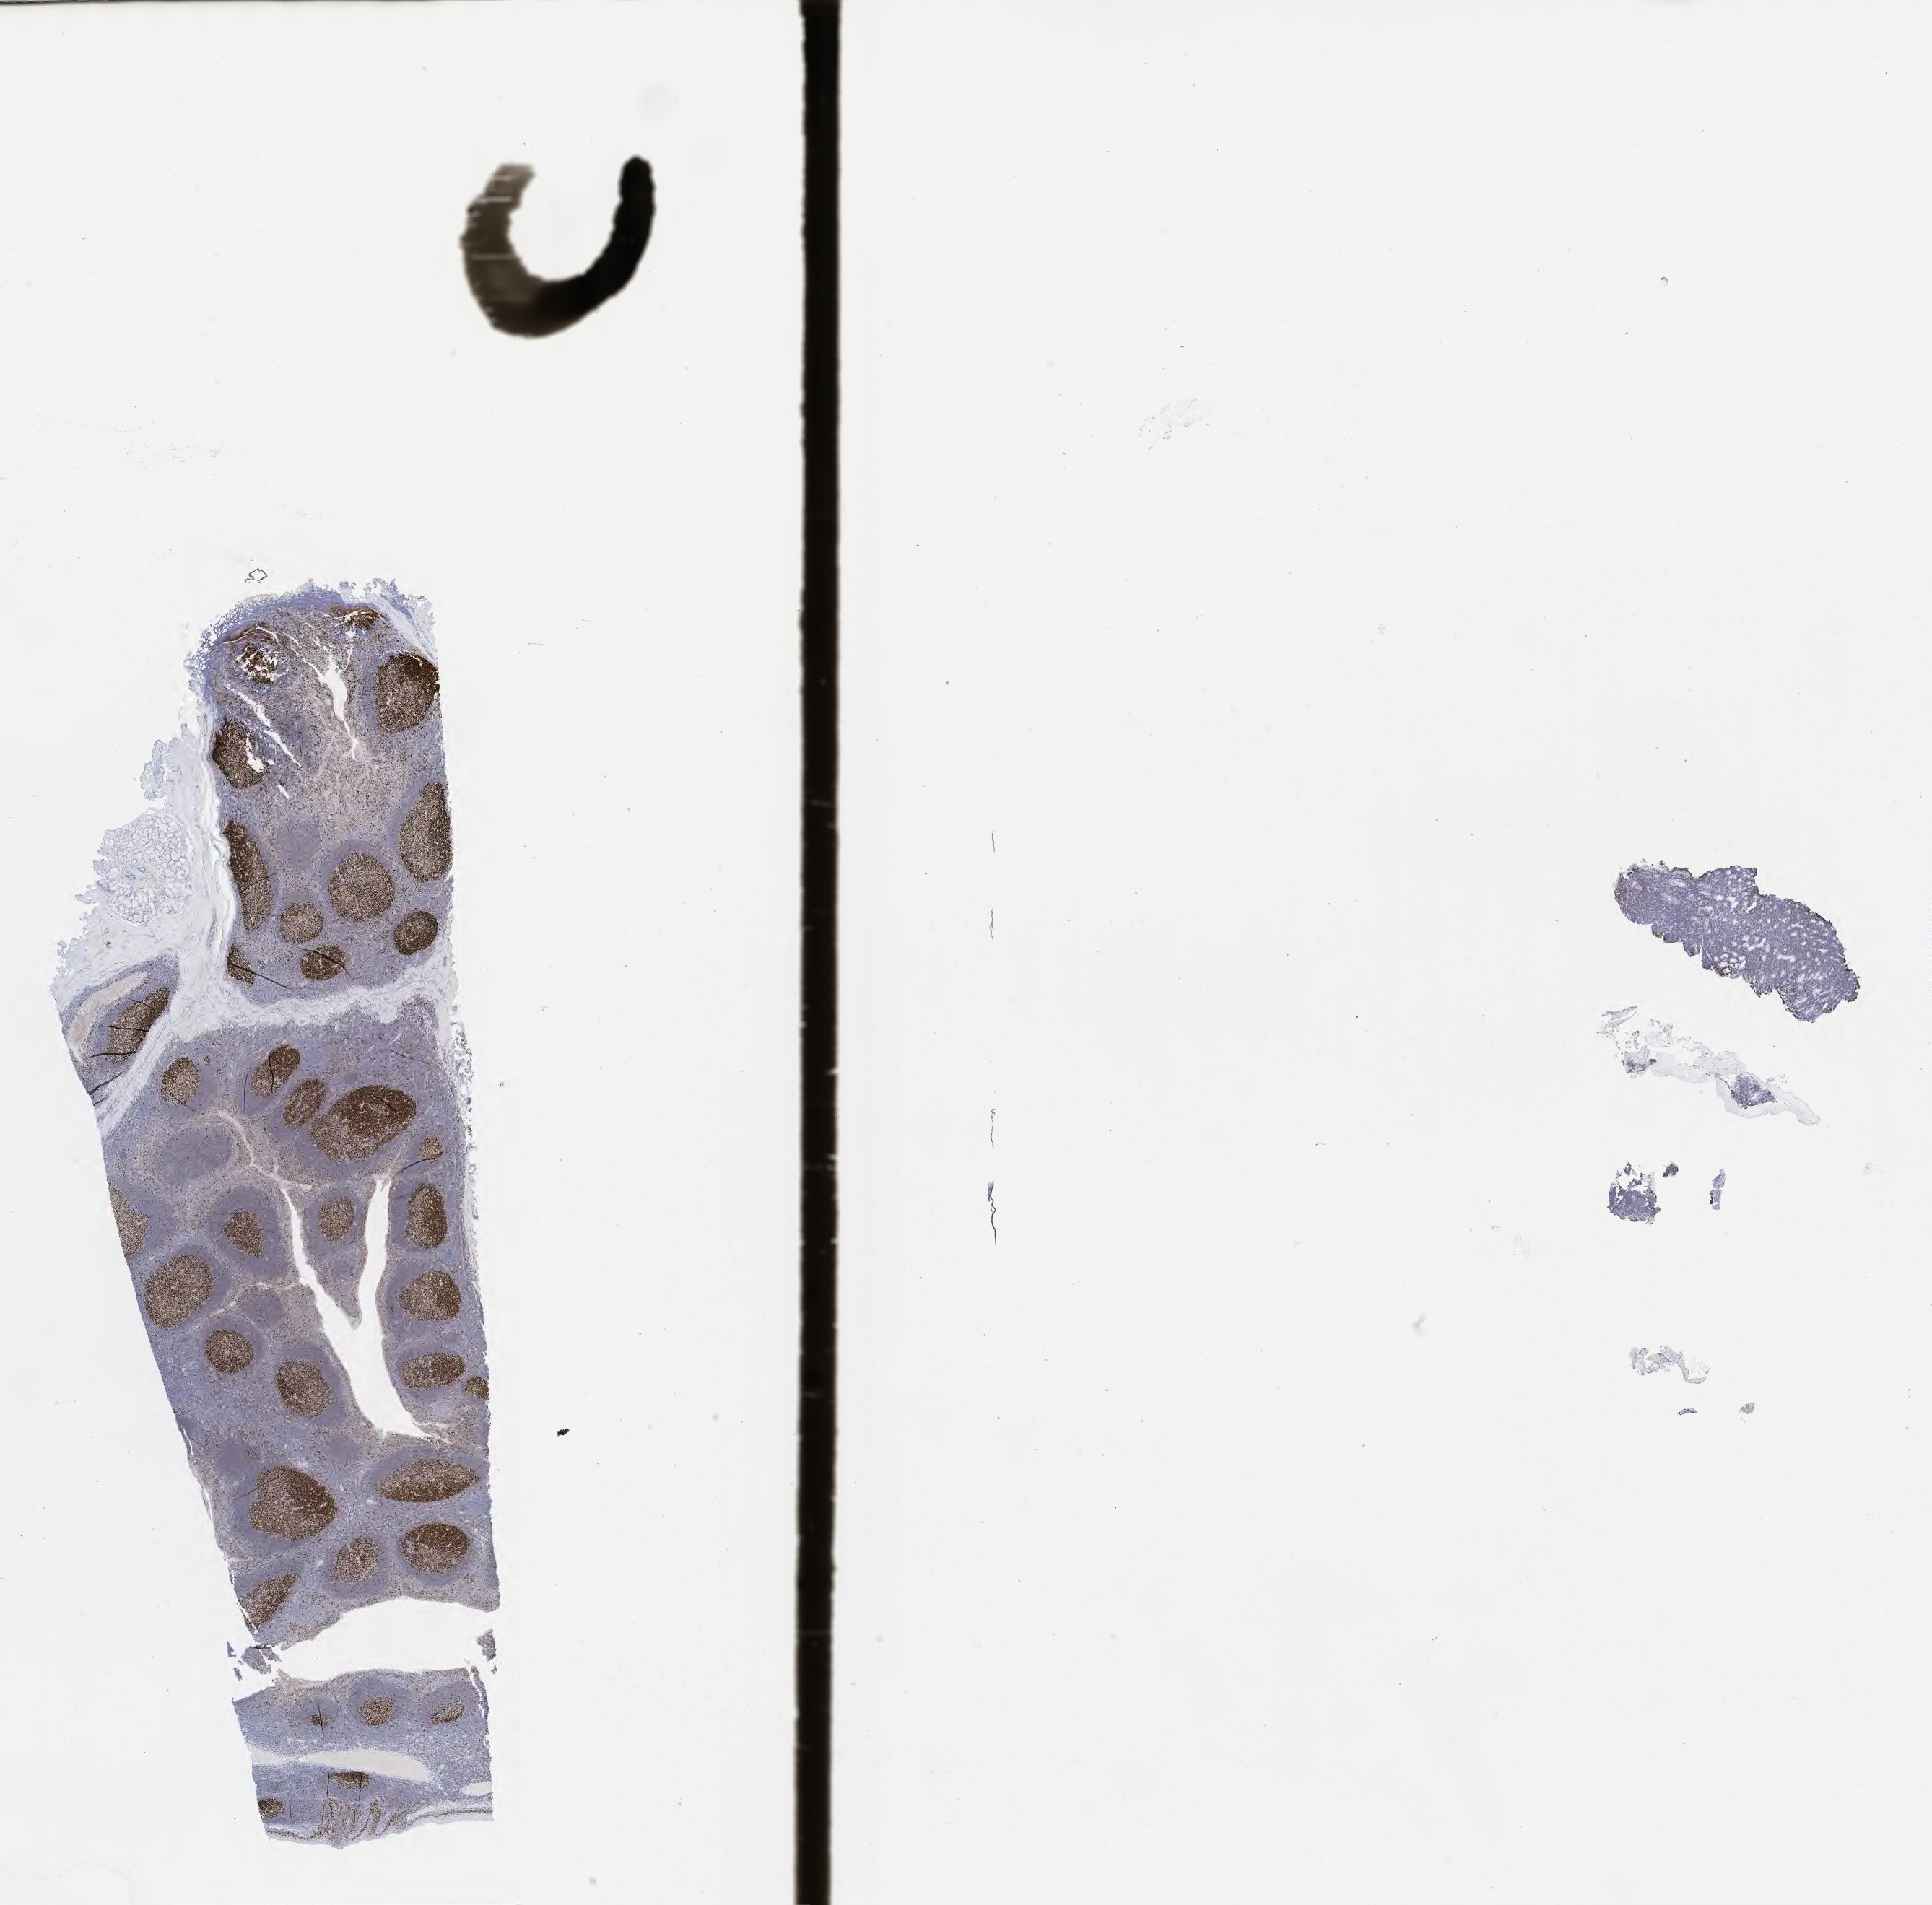
Immunohistochemistry (IHC) whole-slide image stained for Ki-67 — a low-resolution overview of the entire scanned area, about 21.6 x 21.3 mm. Specimen: tumor tissue. Anatomic site: stomach. Female patient, age 28 years.
* histologic diagnosis: Burkitt lymphoma, NOS